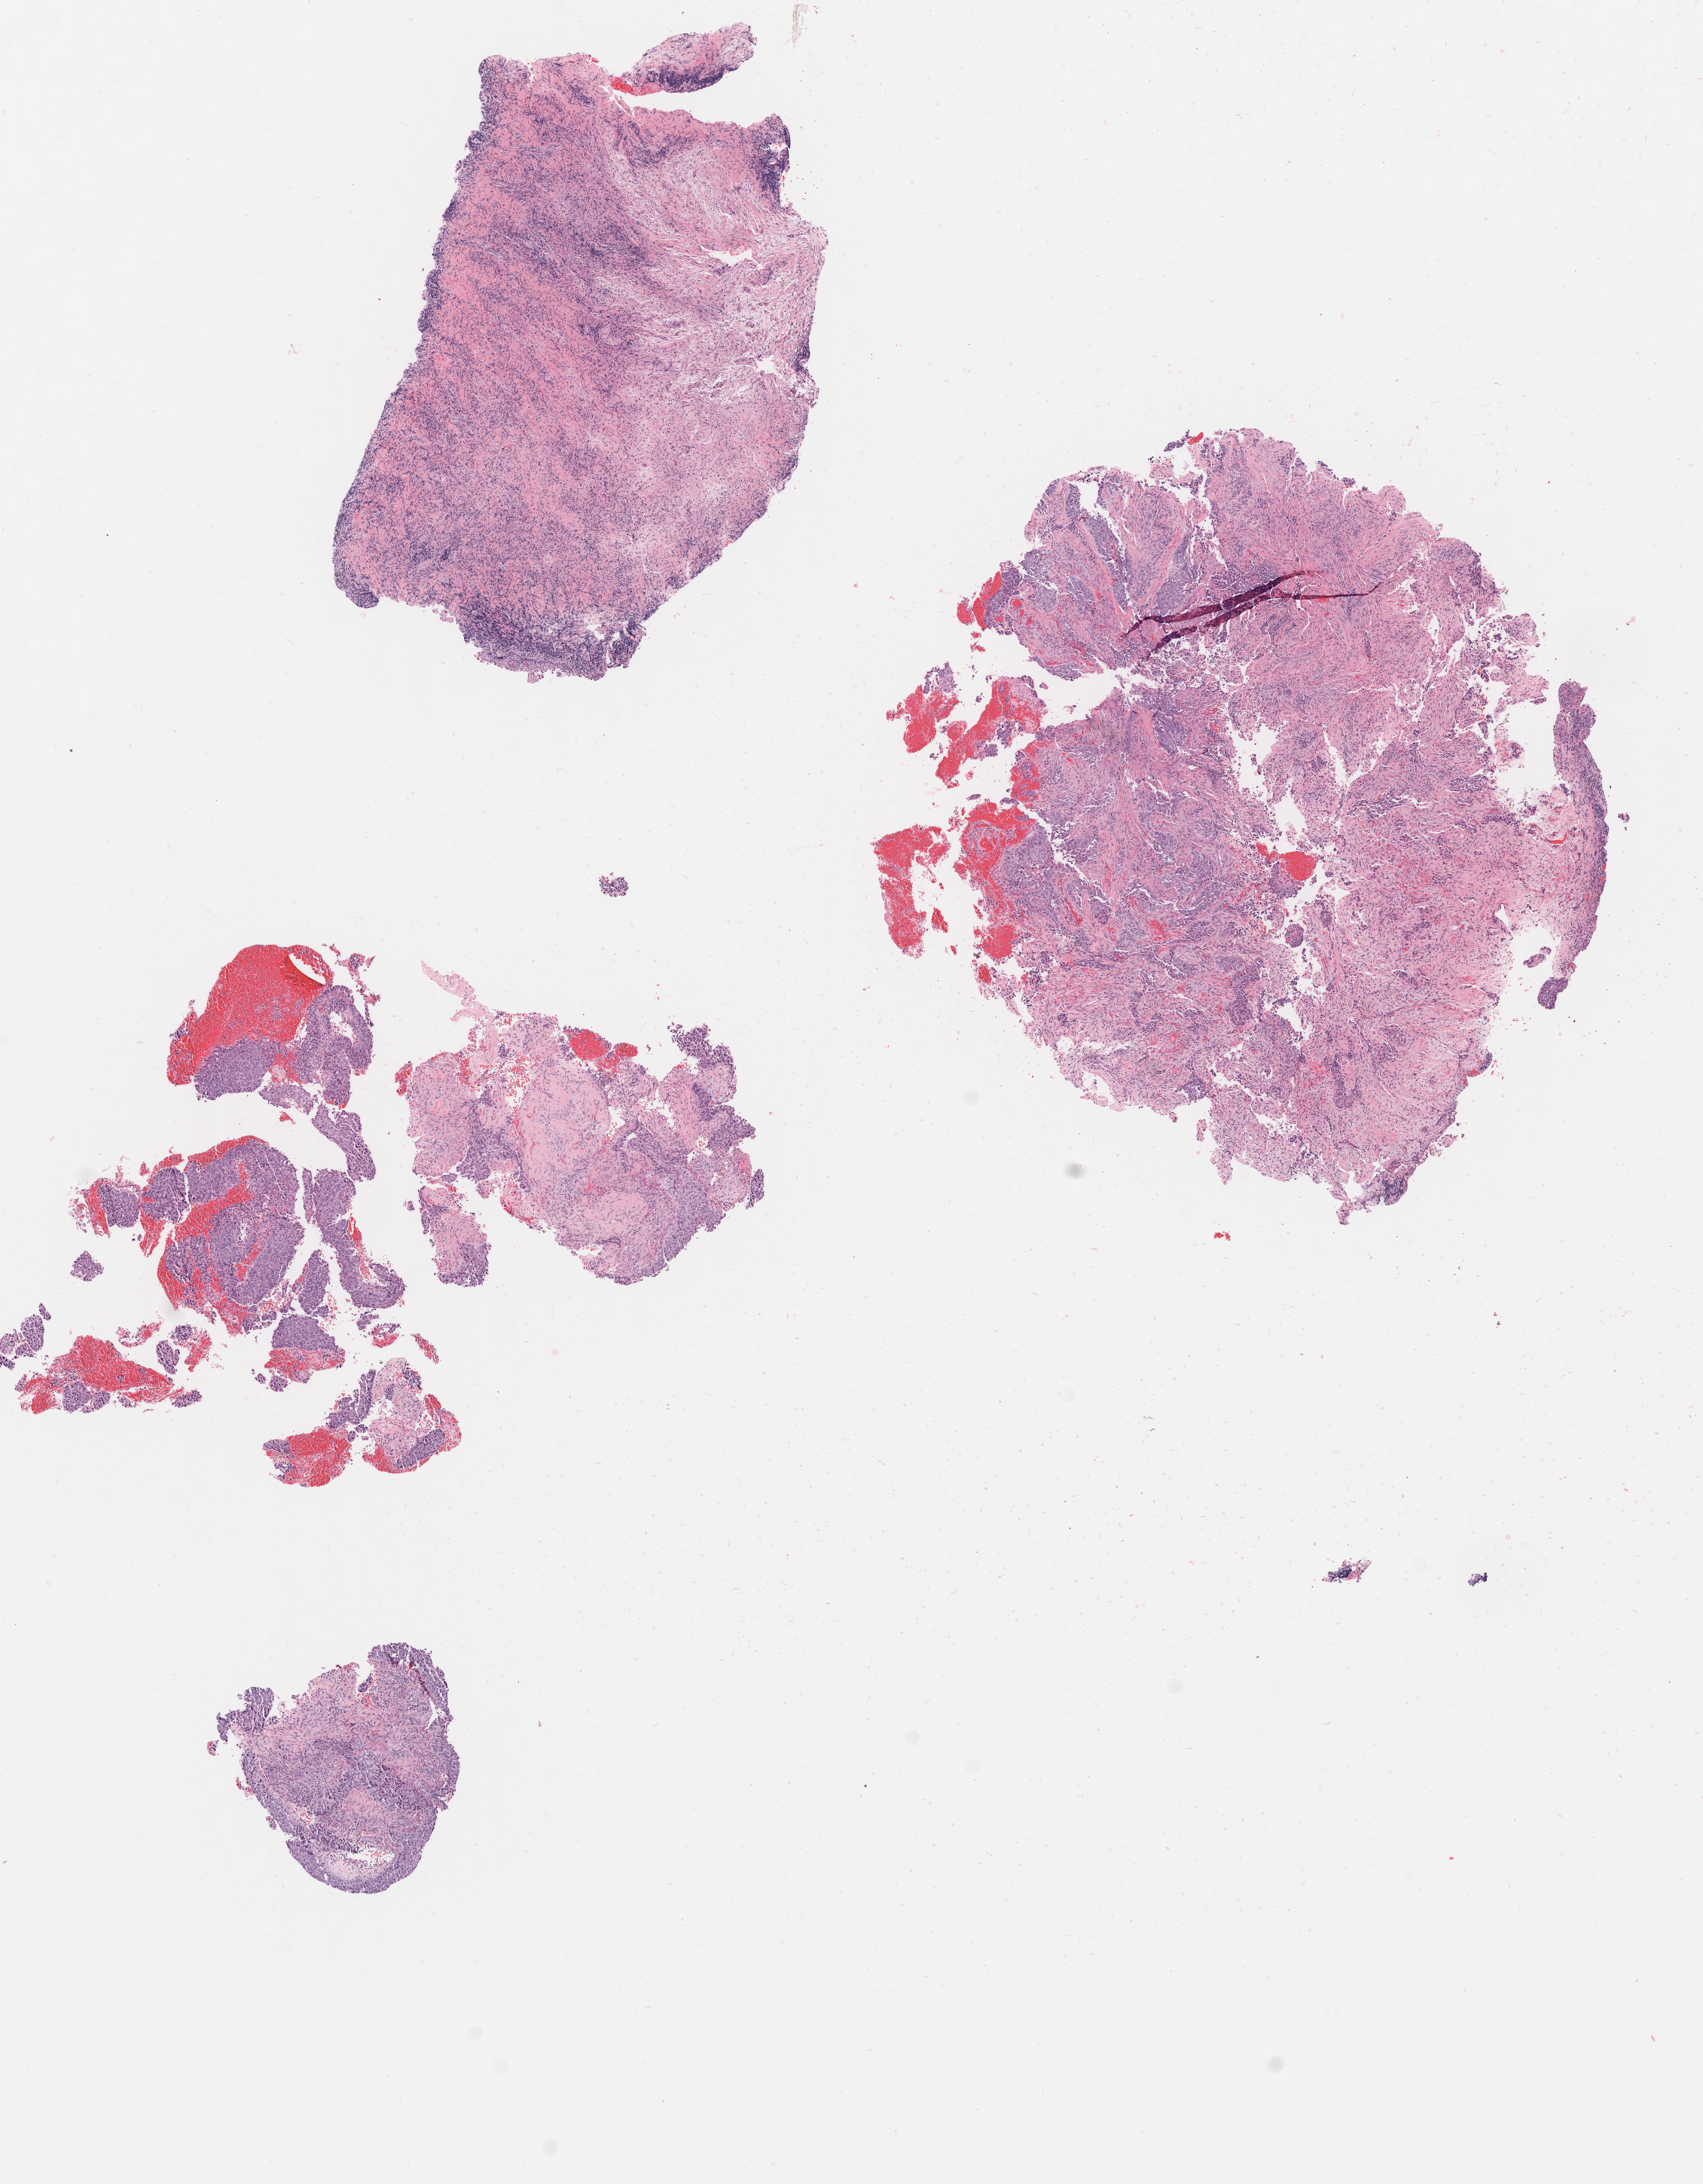
H&E whole-slide image, whole scanned area (about 9.0 x 11.5 mm) shown as a low-resolution overview. Specimen: tumor tissue. Site: cervix. Female patient, aged 54.
* diagnosis: Squamous cell carcinoma, large cell, nonkeratinizing, NOS